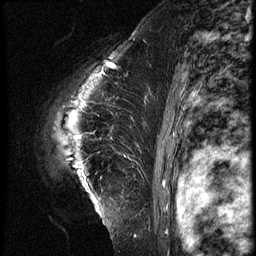
Breast MRI (dynamic contrast-enhanced), one sagittal slice. Slice 47 of 62 in the series (ordered by position). 3 images stored at this slice position (order not interpretable as contrast timing). 1.5 T. TE 4.2 ms, TR 9 ms. 2.5 mm slice thickness. 256 × 256 image matrix, field of view 180 × 180 mm. Female patient, age 39 years. From the clinical record (not read from this slice): setting: breast cancer imaged before/during neoadjuvant chemotherapy; receptor status: HER2-positive.
Annotated regions visible in this slice (semi-automatically segmented with operator editing):
- analysis volume of interest (the breast-tissue region the enhancement analysis was run in; not a lesion): box from (x=36, y=64) to (x=152, y=228) px
- tumour enhancement mask (voxels above the 140 % enhancement threshold inside the analysis volume of interest): (x=77, y=64)–(x=116, y=138)